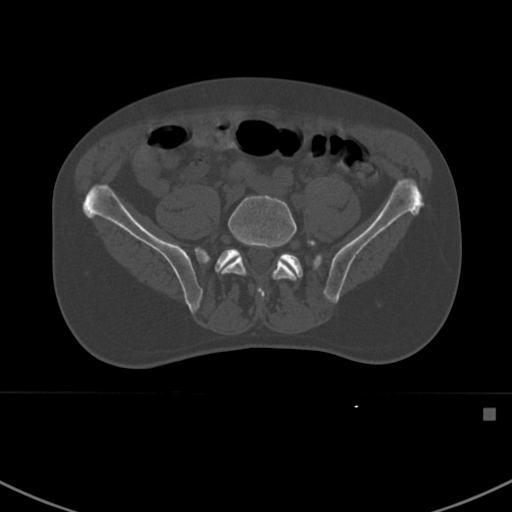
CT including the spine, one axial slice; slice 214 of 412 in the series (ordered by position); reconstruction kernel Br40s; 120 kVp; bone window (W 1800 / L 400 HU); 1.5 mm slice thickness; 512 × 512 image matrix, field of view 358 × 358 mm. Male patient, age 59 years. From the clinical record (not read from this slice): primary cancer: prostate.
Annotated regions visible in this slice (semi-automatically segmented with operator editing):
- L5 vertebra: bounding box [x1, y1, x2, y2] px = [222, 195, 316, 299]